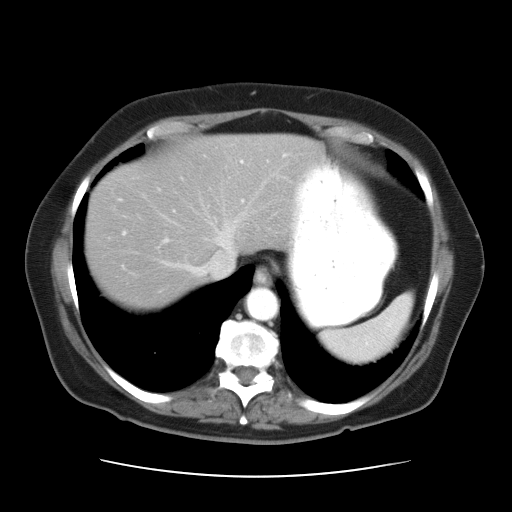
Contrast-enhanced abdominal CT, one axial slice; position 28 of 34 along the scan axis; reconstruction kernel STANDARD; 120 kVp; intravenous contrast given; soft-tissue window (W 400 / L 40 HU); 7.5 mm slice thickness; 512 × 512 image matrix, field of view 360 × 360 mm. Female patient, age 65 years. Case-level facts recorded for this patient, not image findings: diagnosis: colorectal cancer liver metastases, imaged before liver resection; multiple liver metastases: yes; largest metastasis: 2.2 cm; chemotherapy before resection: yes.
Structures marked on this image (outlined manually by an expert reader):
- hepatic veins: bounding box (x1, y1, x2, y2) in pixels: (117, 172, 287, 278)
- liver: (88, 136, 314, 302)
- planned liver remnant (the part of the liver to remain after resection): (88, 136, 313, 304)
- portal vein (with intrahepatic branches): (124, 159, 248, 234)